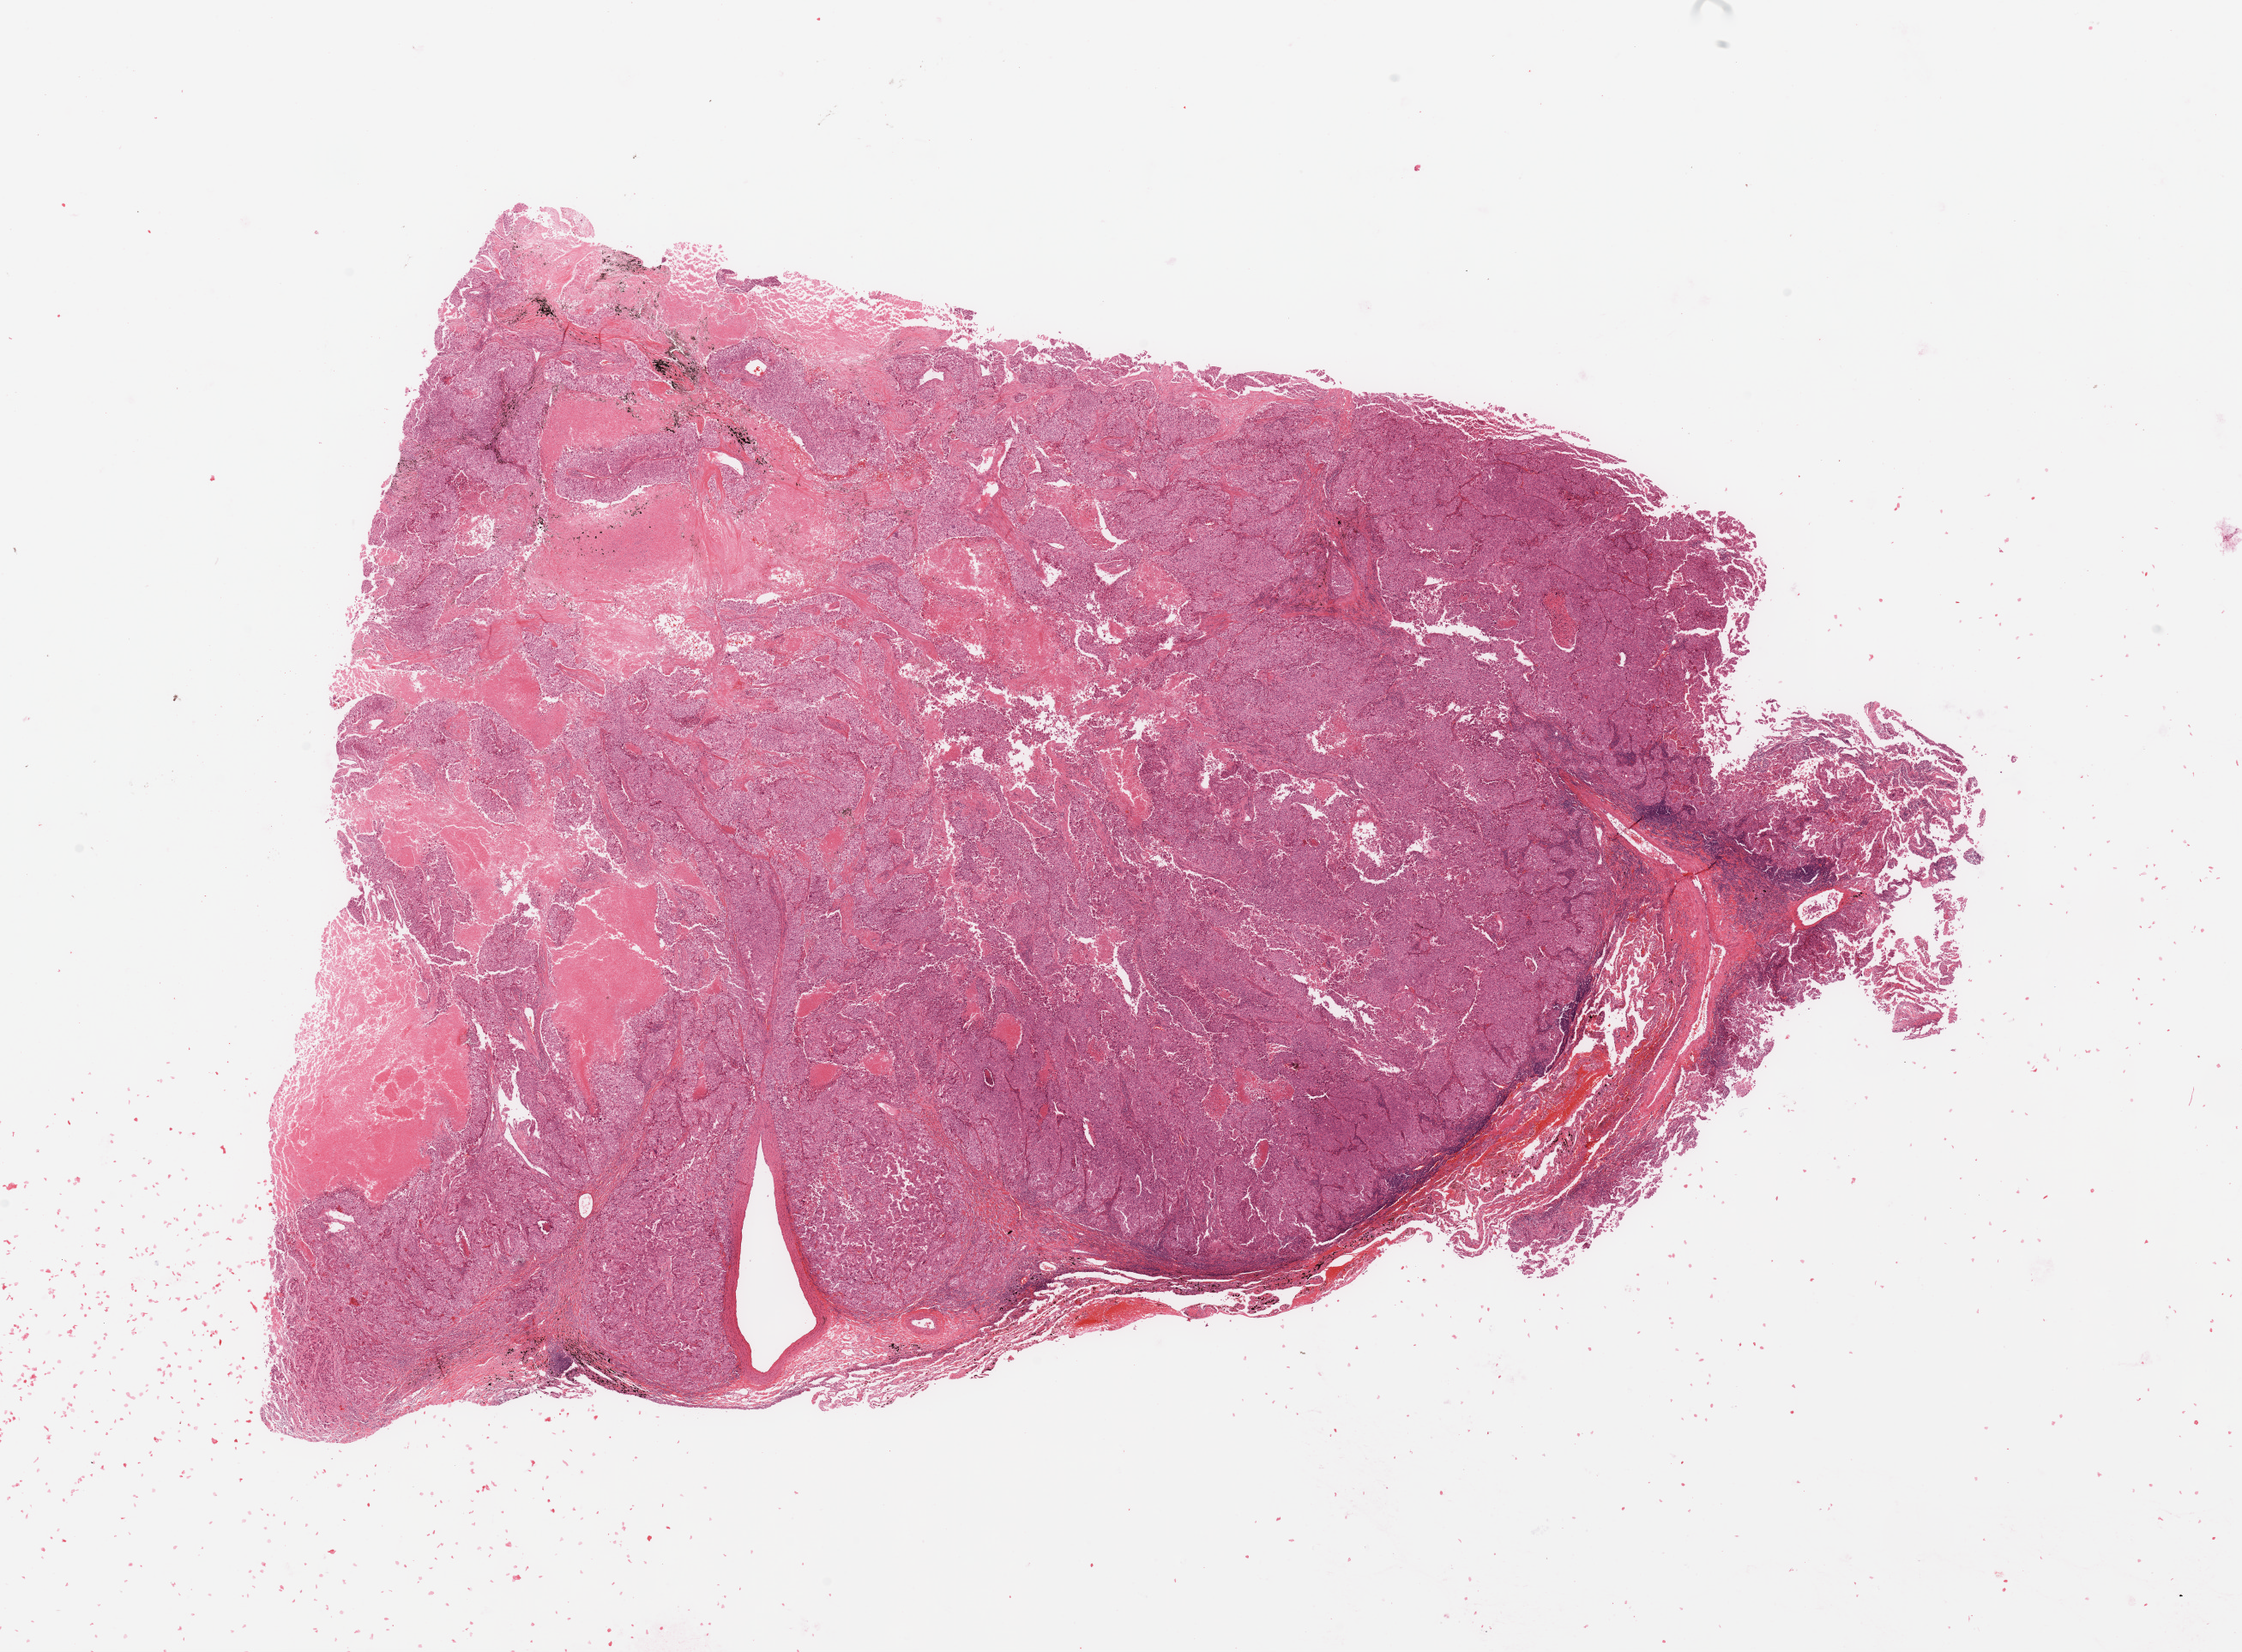
Digitized H&E tissue section (whole slide), whole scanned area (about 20.7 x 15.2 mm, slide scanned at 20x) shown as a low-resolution overview; tumour tissue sample, sampled site: lung. Patient: male, age 59 years.
Diagnosis: Adenocarcinoma, NOS.